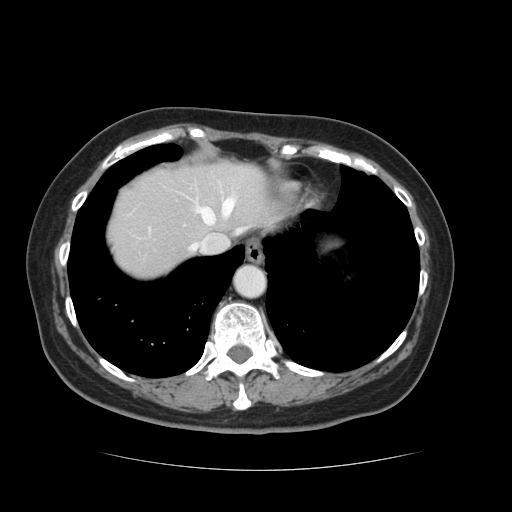
Contrast-enhanced abdominal CT, one axial slice. Position 110 of 128 along the scan axis. 120 kVp. Intravenous contrast given. Soft-tissue window (W 400 / L 40 HU). 2.5 mm slice thickness. 512 × 512 image matrix, field of view 366 × 366 mm. Female patient, age 67 years. Case-level facts recorded for this patient, not image findings: diagnosis: colorectal cancer liver metastases, imaged before liver resection; multiple liver metastases: yes; largest metastasis: 3 cm; chemotherapy before resection: no.
Annotated regions visible in this slice (outlined manually by an expert reader):
- hepatic veins: box from (x=188, y=197) to (x=246, y=252) px
- liver: (x=107, y=159)–(x=274, y=278)
- planned liver remnant (the part of the liver to remain after resection): (x=107, y=162)–(x=275, y=278)